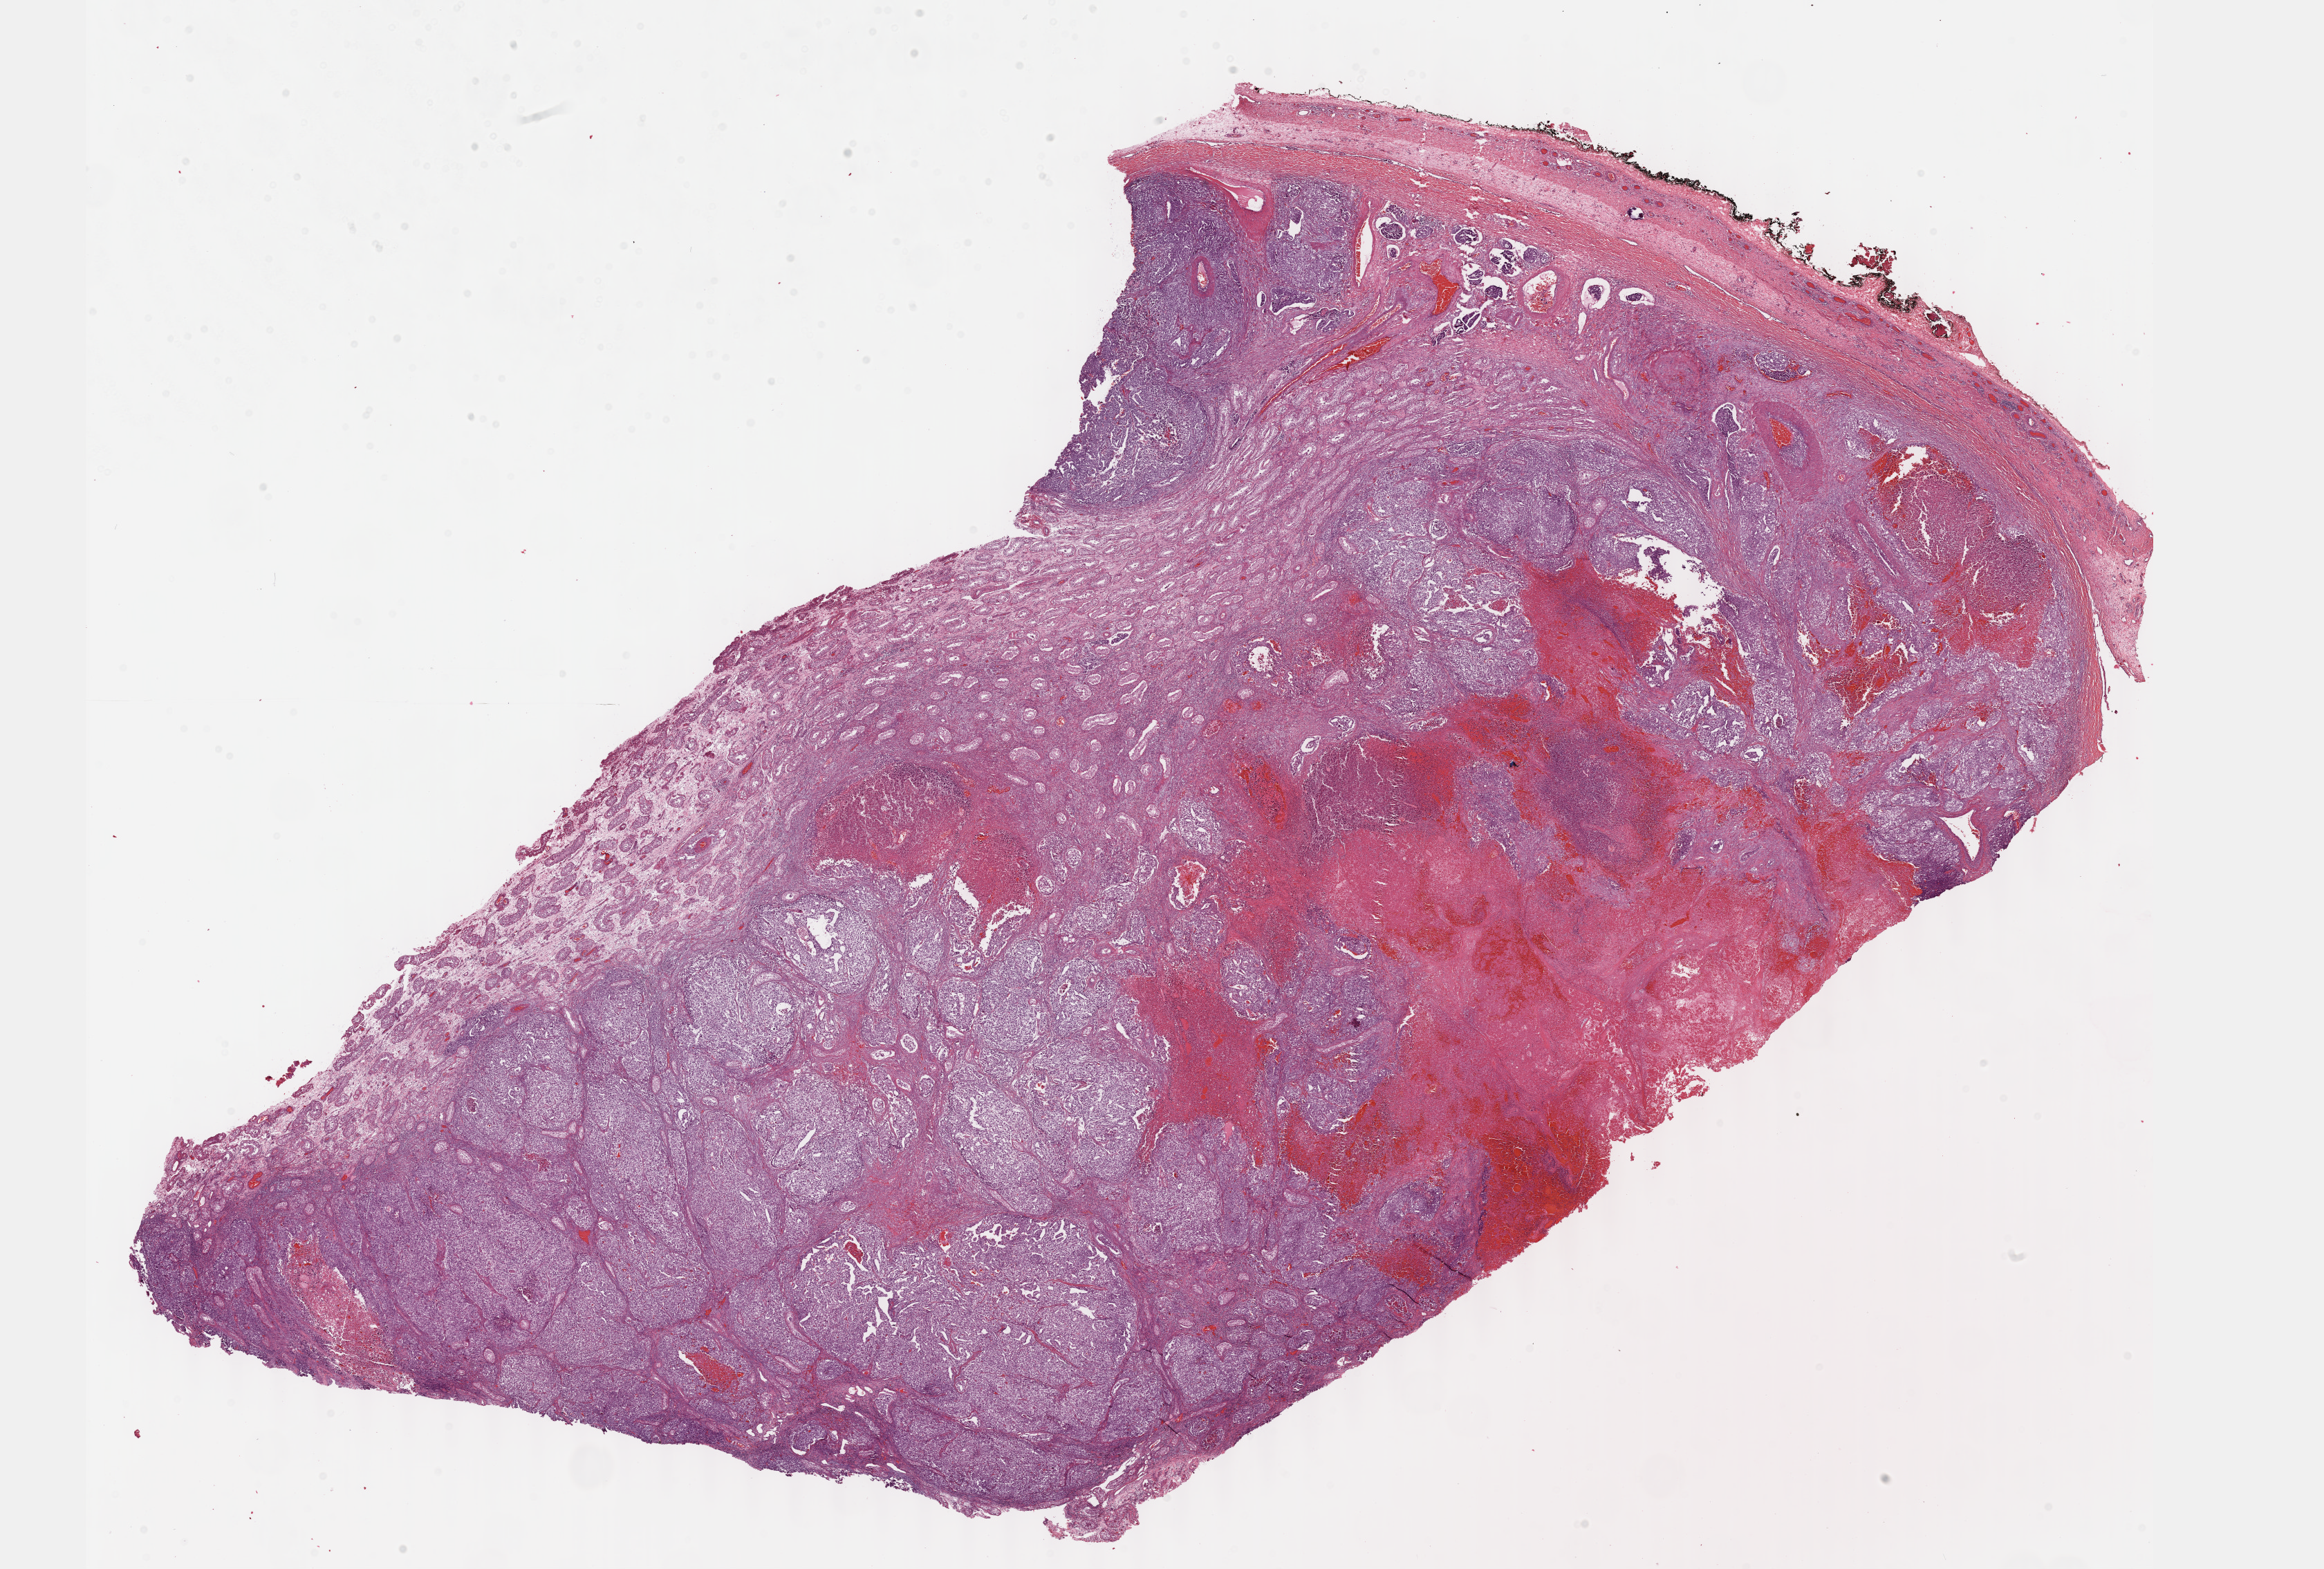
H&E whole-slide image — shown as a low-resolution overview of the whole scanned area (about 27.2 x 18.3 mm), FFPE section, sample: primary tumour, testis. Male patient; age at initial diagnosis 24 years.
Diagnosis: Embryonal carcinoma, NOS. AJCC pathologic stage: IS. Laterality: right.